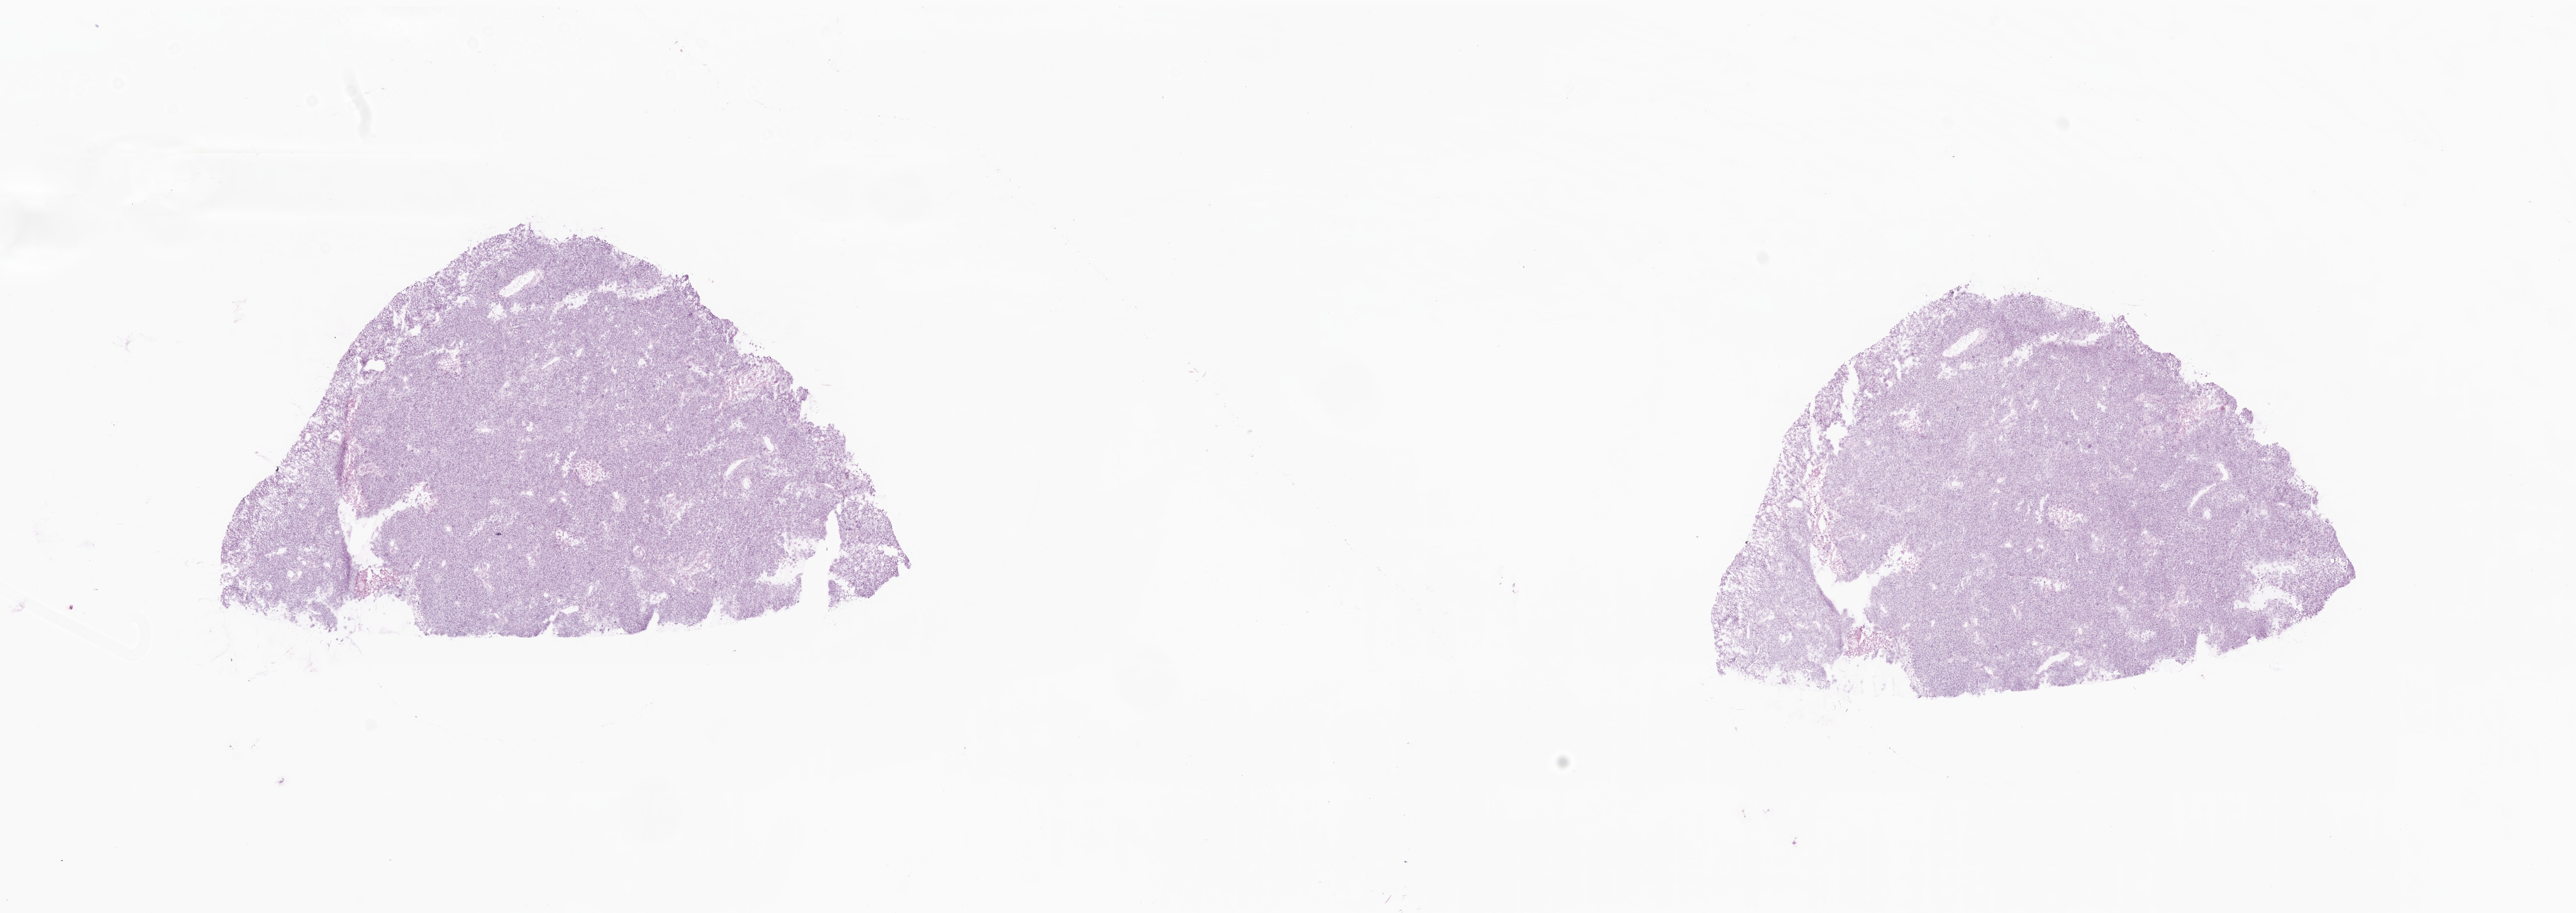
Digitized haematoxylin and eosin-stained section, low-resolution overview of the scanned area, about 21.5 x 7.6 mm. Cryosection. Metastatic tumor tissue, resected from lymph node. Female, age 53 years at initial diagnosis. Composition of this section per pathologist review: tumor cells 90%, tumor nuclei 90%, stromal cells 10%, necrosis 0%, normal cells 0%. Inflammatory infiltration, as recorded: lymphocyte infiltration 3%, monocyte infiltration 1%, neutrophil infiltration 2%.
Patient diagnosis (primary): Malignant melanoma, NOS. Section: top of the tissue portion.